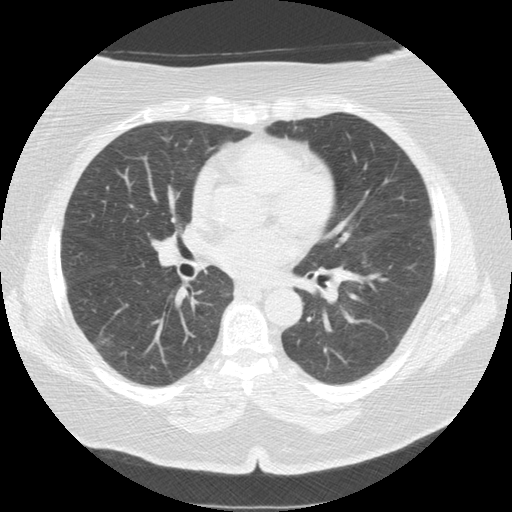
Axial slice from a low-dose chest CT screening exam. Baseline annual screen. Lung window (W 1500 / L -600 HU). 2.5 mm slice thickness. Slice 75 of 161 in the series. Female, age 65 years at enrolment. Current smoker at enrolment.
Lesion marked by an expert reader, bounding box <349,247,377,274> (left, top, right, bottom; pixels). Screening reader's record for this exam: no non-calcified nodule ≥4 mm recorded. Official screen result: negative screen, minor abnormalities not suspicious for lung cancer. Participant outcome: lung cancer diagnosed 986 days after this screen — adenocarcinoma, NOS, left lower lobe, moderately differentiated (G2), stage IA (AJCC 6th edition), 12 mm at pathology.